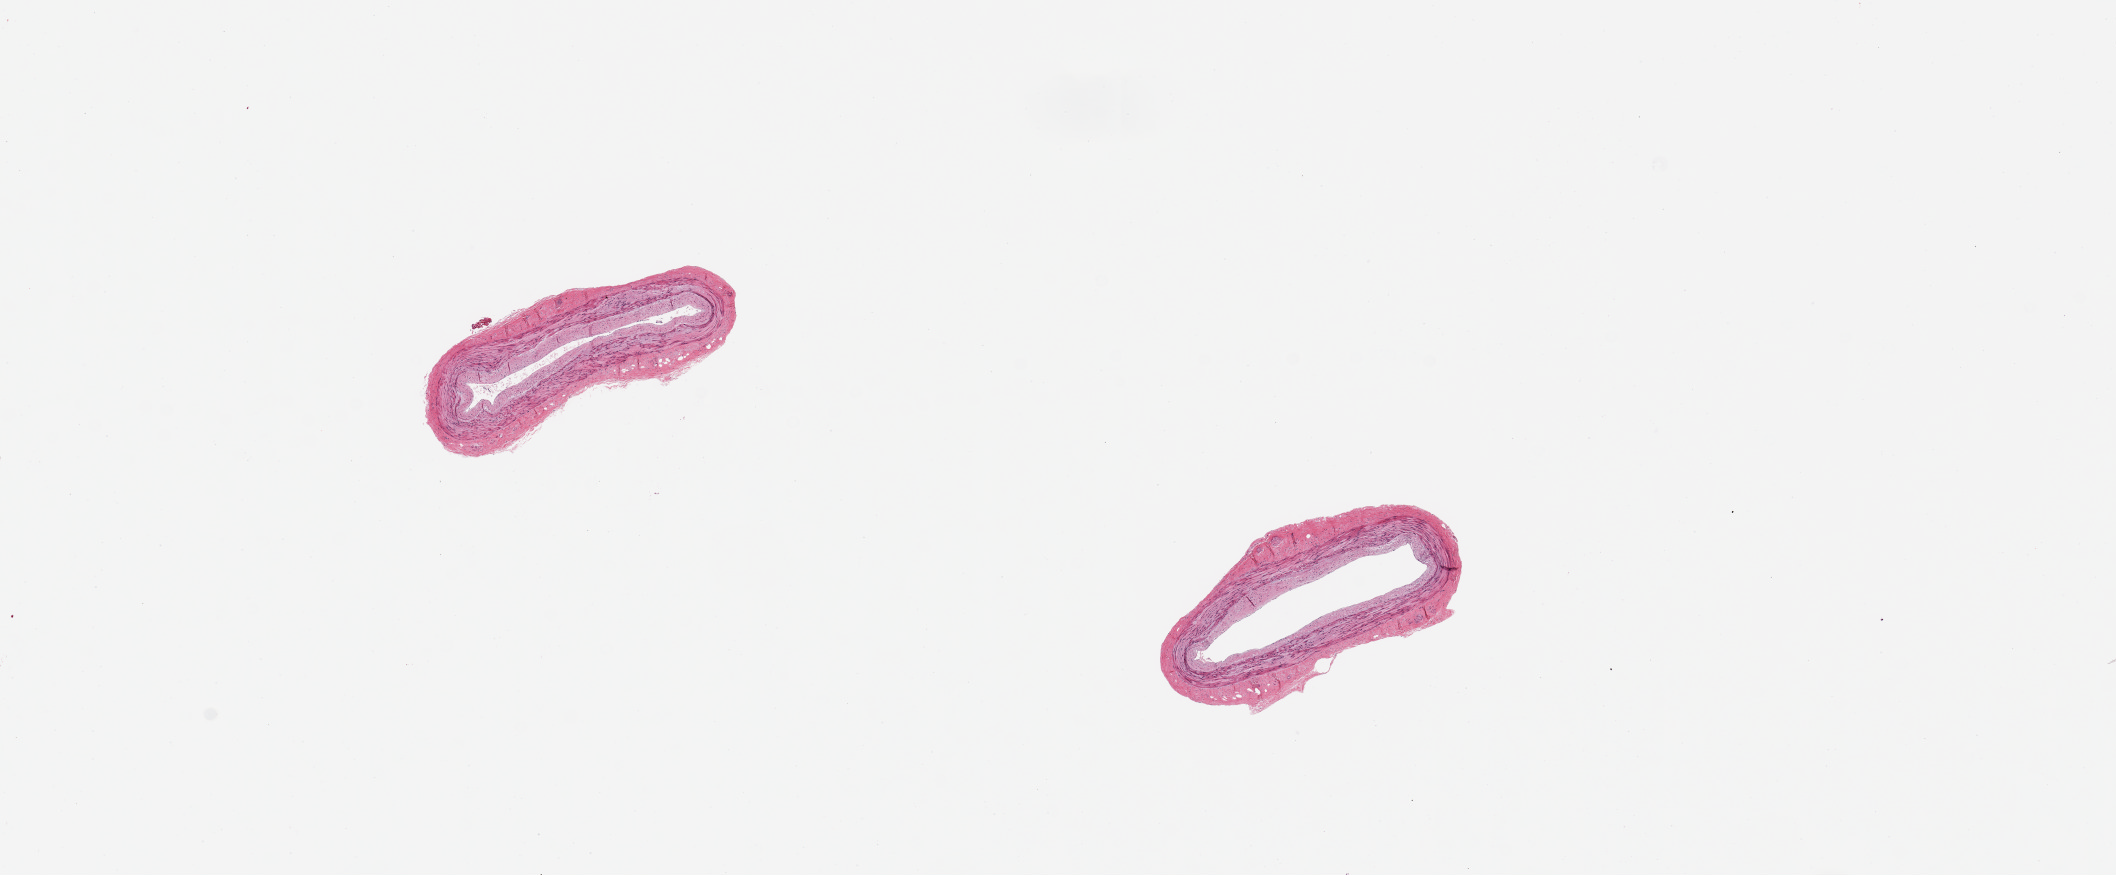
Digitized H&E-stained section, brightfield — a low-resolution overview of the entire scanned area, about 16.7 x 6.9 mm. PAXgene-fixed paraffin-embedded (PFPE) section. Target tissue: tibial artery. Donor tissue sample. Donor sex: female.
Pathologist's review note for this sample: 2 pieces, 3x1 & 2.5x1mm; good clean specimens.